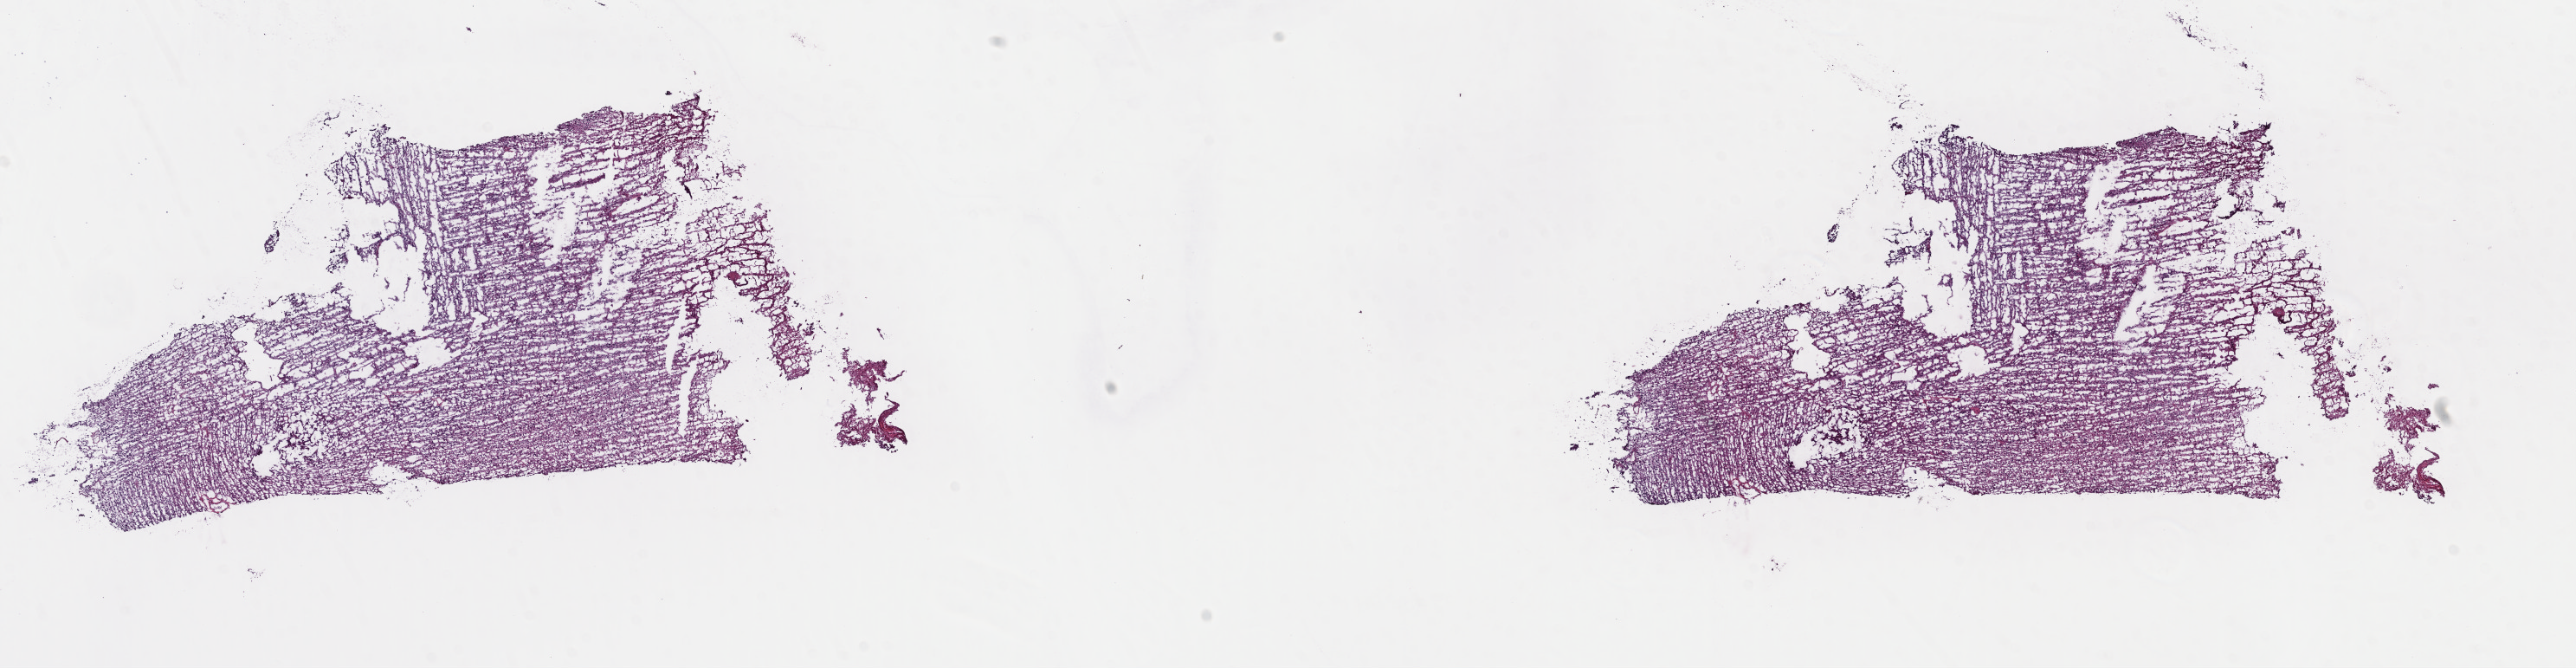
H&E whole-slide image — whole scanned area (about 23.4 x 6.1 mm) shown as a low-resolution overview. Frozen section from the top of the tissue portion. Primary tumour sample from the brain. Male, age 39 years at initial diagnosis. Histologic grade: G3 (poorly differentiated). Composition of this section per pathologist review: tumour cells 50%, tumour nuclei 85%, normal cells 10%, stromal cells 40%, necrosis 0%. Infiltration values recorded for this section: lymphocyte infiltration 0%, monocyte infiltration 0%, neutrophil infiltration 0%.
* diagnosis: Astrocytoma, anaplastic (cerebrum)
* laterality: left